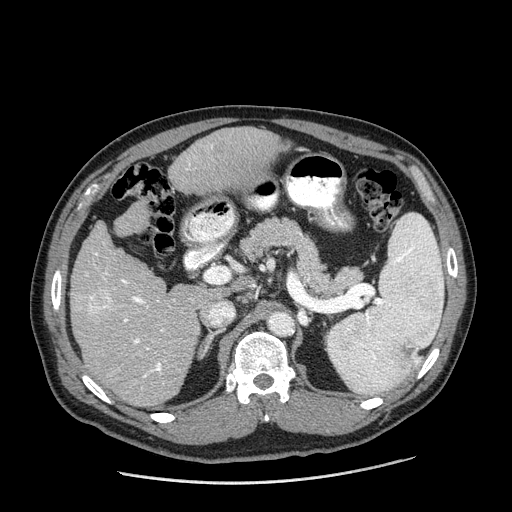
Contrast-enhanced abdominal CT (liver protocol), one axial slice; slice 103 of 198 in the series (ordered by position); reconstruction kernel STANDARD; 120 kVp; one of 2 acquisitions stored at this slice position; soft-tissue window (W 400 / L 40 HU); 2.5 mm slice thickness; 512 × 512 image matrix, field of view 400 × 400 mm. Case-level facts recorded for this patient, not image findings: diagnosis: hepatocellular carcinoma (patient treated with transarterial chemoembolisation; whether this scan precedes or follows treatment is not stated here); TNM stage (as recorded): Stage-II; Child-Pugh class: A; tumour differentiation: moderately differentiated; tumour nodularity: multinodular.
Outlined on this slice (semi-automatic segmentation, software-assisted and operator-edited):
- liver parenchyma outside the tumour (the mass and vessels are separate outlines, so this box may not span the whole liver): bounding box (x1, y1, x2, y2) in pixels: (70, 126, 290, 406)
- mass: (87, 288, 116, 315)
- liver vessels: (94, 147, 213, 378)